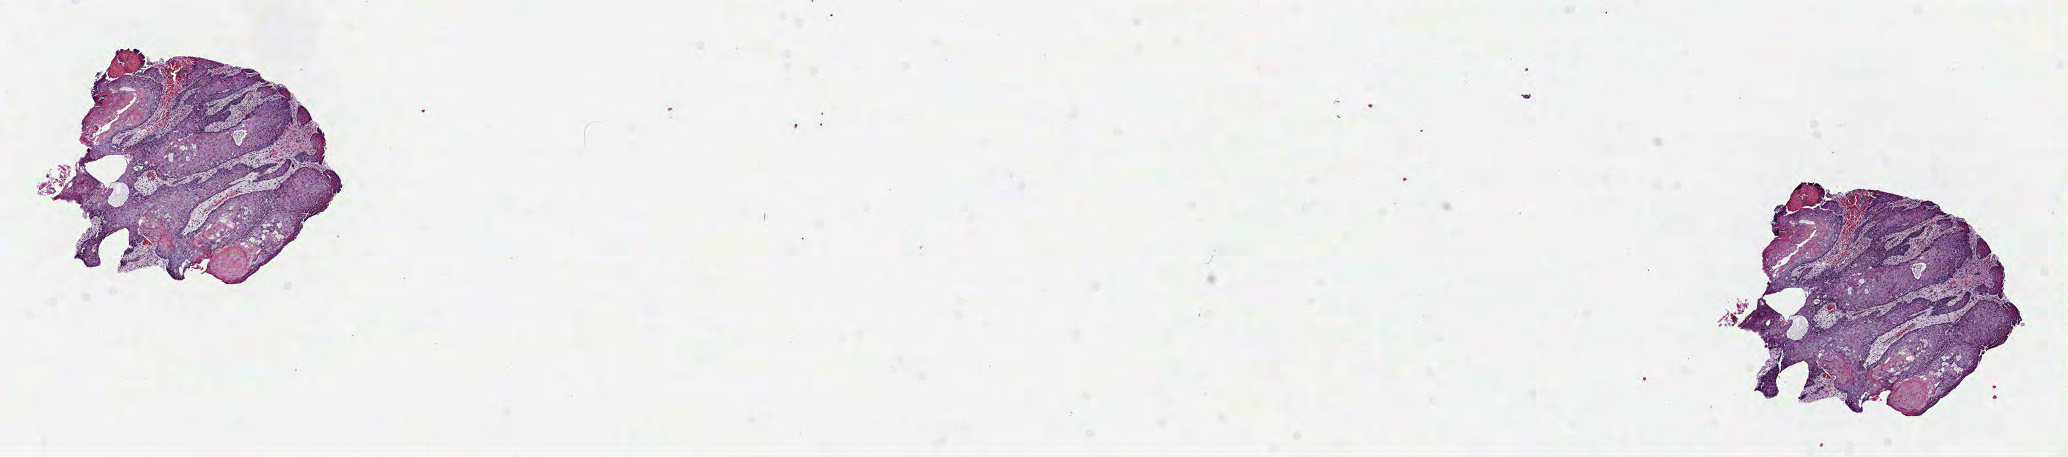
Digitized H&E-stained tissue section (whole slide) — a low-resolution overview of the entire scanned area, about 16.7 x 3.7 mm (from a 40x scan), formalin-fixed paraffin-embedded (FFPE) diagnostic section, primary tumour sample from the head and neck. Male, age 68 years at initial diagnosis. Histologic grade: G2 (moderately differentiated).
AJCC pathologic stage: IVA (7th edition). TNM: T3 N2b. Lymph nodes positive (case pathology): 6 of 14 examined. Pathologic diagnosis: Squamous cell carcinoma, NOS (cheek mucosa).